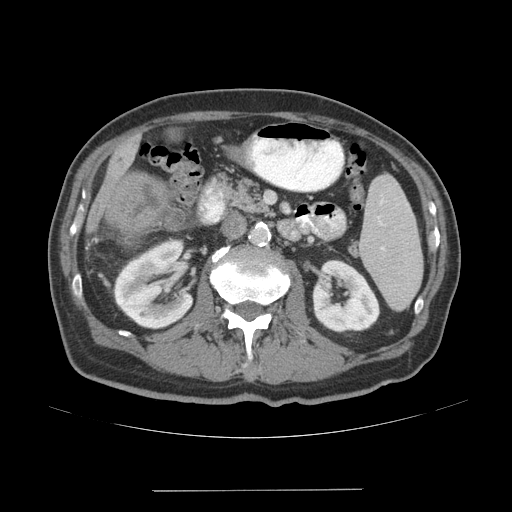
Contrast-enhanced abdominal CT (liver protocol), one axial slice. Reconstruction kernel STANDARD. 140 kVp. Soft-tissue window (W 400 / L 40 HU). 2.5 mm slice thickness. 512 × 512 image matrix, field of view 400 × 400 mm. From the clinical record (not read from this slice): diagnosis: hepatocellular carcinoma (patient treated with transarterial chemoembolisation; whether this scan precedes or follows treatment is not stated here); TNM stage (as recorded): Stage-IVA.
Structures marked on this image (semi-automatically segmented with operator editing):
- liver parenchyma outside the tumour (the mass and vessels are separate outlines, so this box may not span the whole liver): bounding box [x1, y1, x2, y2] px = [86, 139, 138, 252]
- mass: [106, 173, 173, 237]